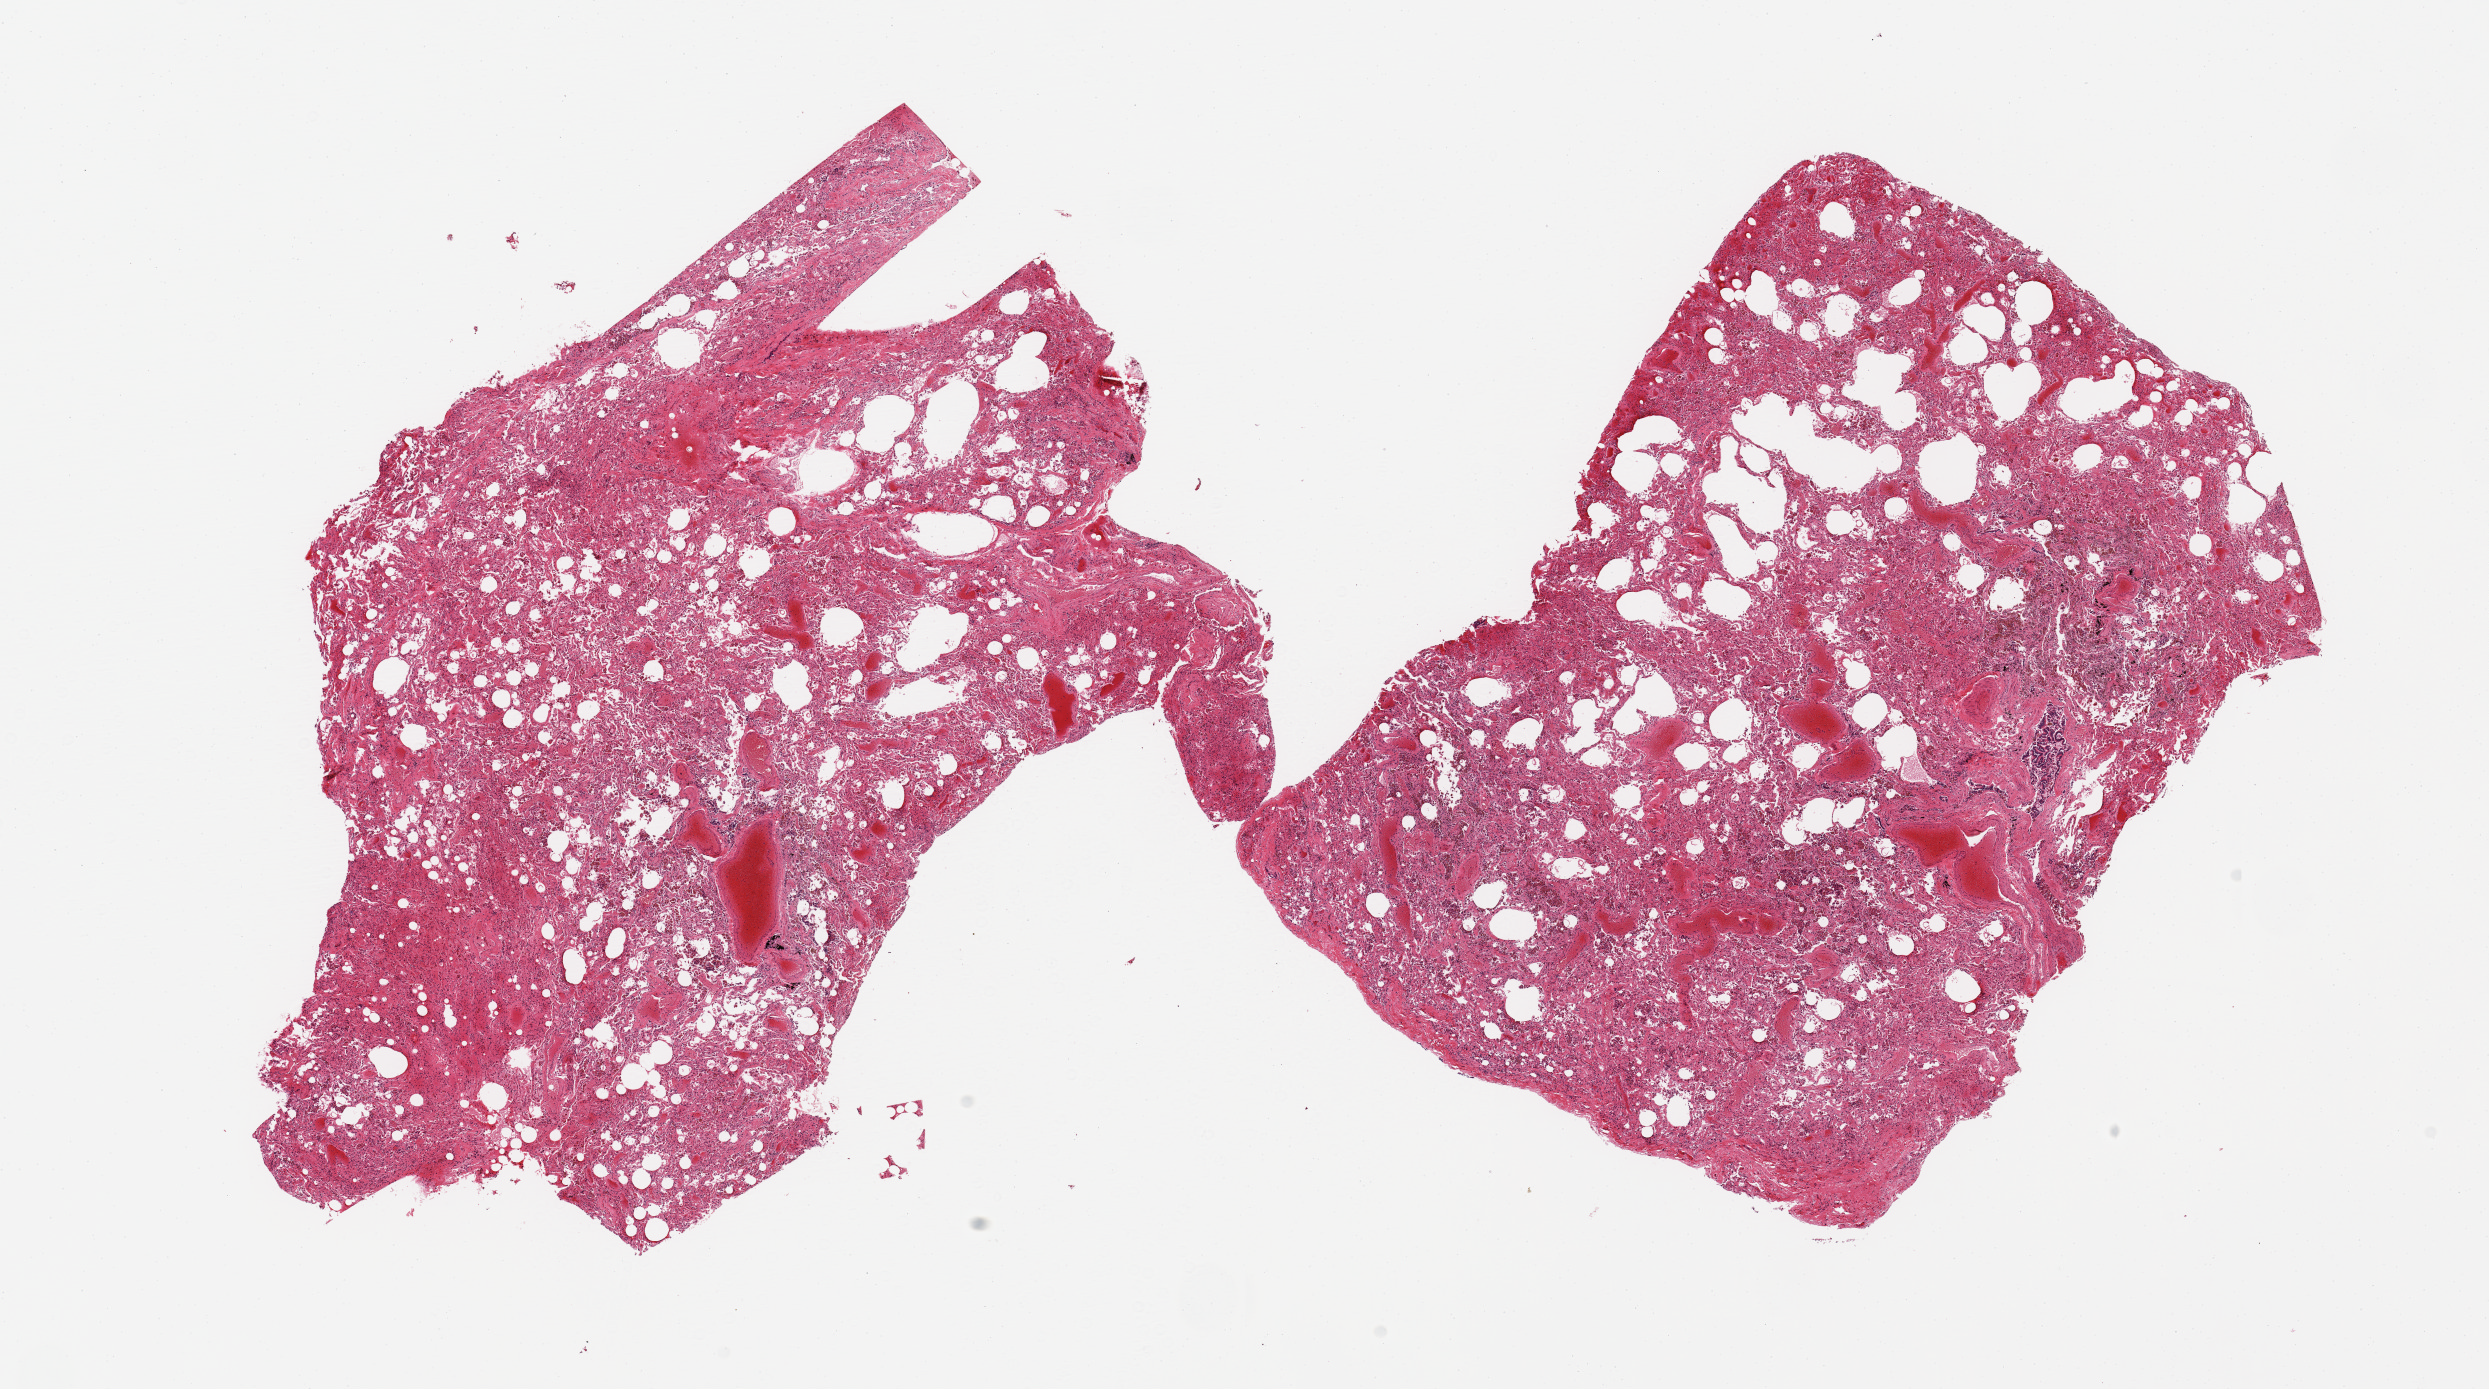
Whole-slide image, haematoxylin and eosin stain — low-resolution overview of the scanned area, about 19.7 x 11.0 mm (acquisition: 20x scan); PAXgene-fixed, paraffin-embedded tissue; sampled site (target tissue): lung; donor tissue sample. Donor sex: female.
Review note (as recorded): 2 pieces, moderate congestion, evidence chronic congestion.